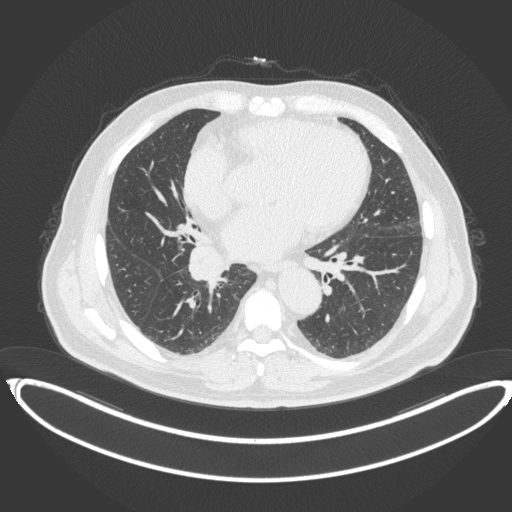
Chest CT, one axial slice. Reconstruction kernel B31f. 120 kVp. Lung window (W 1500 / L -600 HU). 1 mm slice thickness. 512 × 512 image matrix, field of view 448 × 448 mm. Male patient, age 61 years. From the clinical record (not read from this slice): clinical TNM (as recorded): T1b N1 M0.
Annotated regions visible in this slice (bounding box drawn by a radiologist):
- lung tumour (recorded histology: squamous cell carcinoma): bounding box (x1, y1, x2, y2) in pixels: (184, 244, 231, 293)